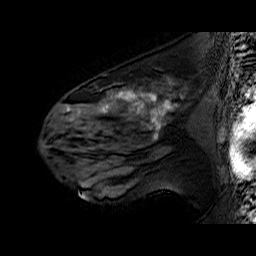
Breast MRI (dynamic contrast-enhanced), one sagittal slice. Position 36 of 60 along the scan axis. Dynamic contrast-enhanced series, time point 2 of 6 at this slice position (early post-contrast). 1.5 T. TE 6.4 ms, TR 32.9 ms. 256 × 256 image matrix, field of view 200 × 200 mm. Female patient. From the clinical record (not read from this slice): setting: breast cancer imaged before/during neoadjuvant chemotherapy; receptor status: HER2-positive.
Outlined on this slice (semi-automatic segmentation, software-assisted and operator-edited):
- analysis volume of interest (the breast-tissue region the enhancement analysis was run in; not a lesion): box from (x=51, y=78) to (x=196, y=160) px
- tumour enhancement mask (voxels above the 100 % enhancement threshold inside the analysis volume of interest): (x=67, y=90)–(x=173, y=138)